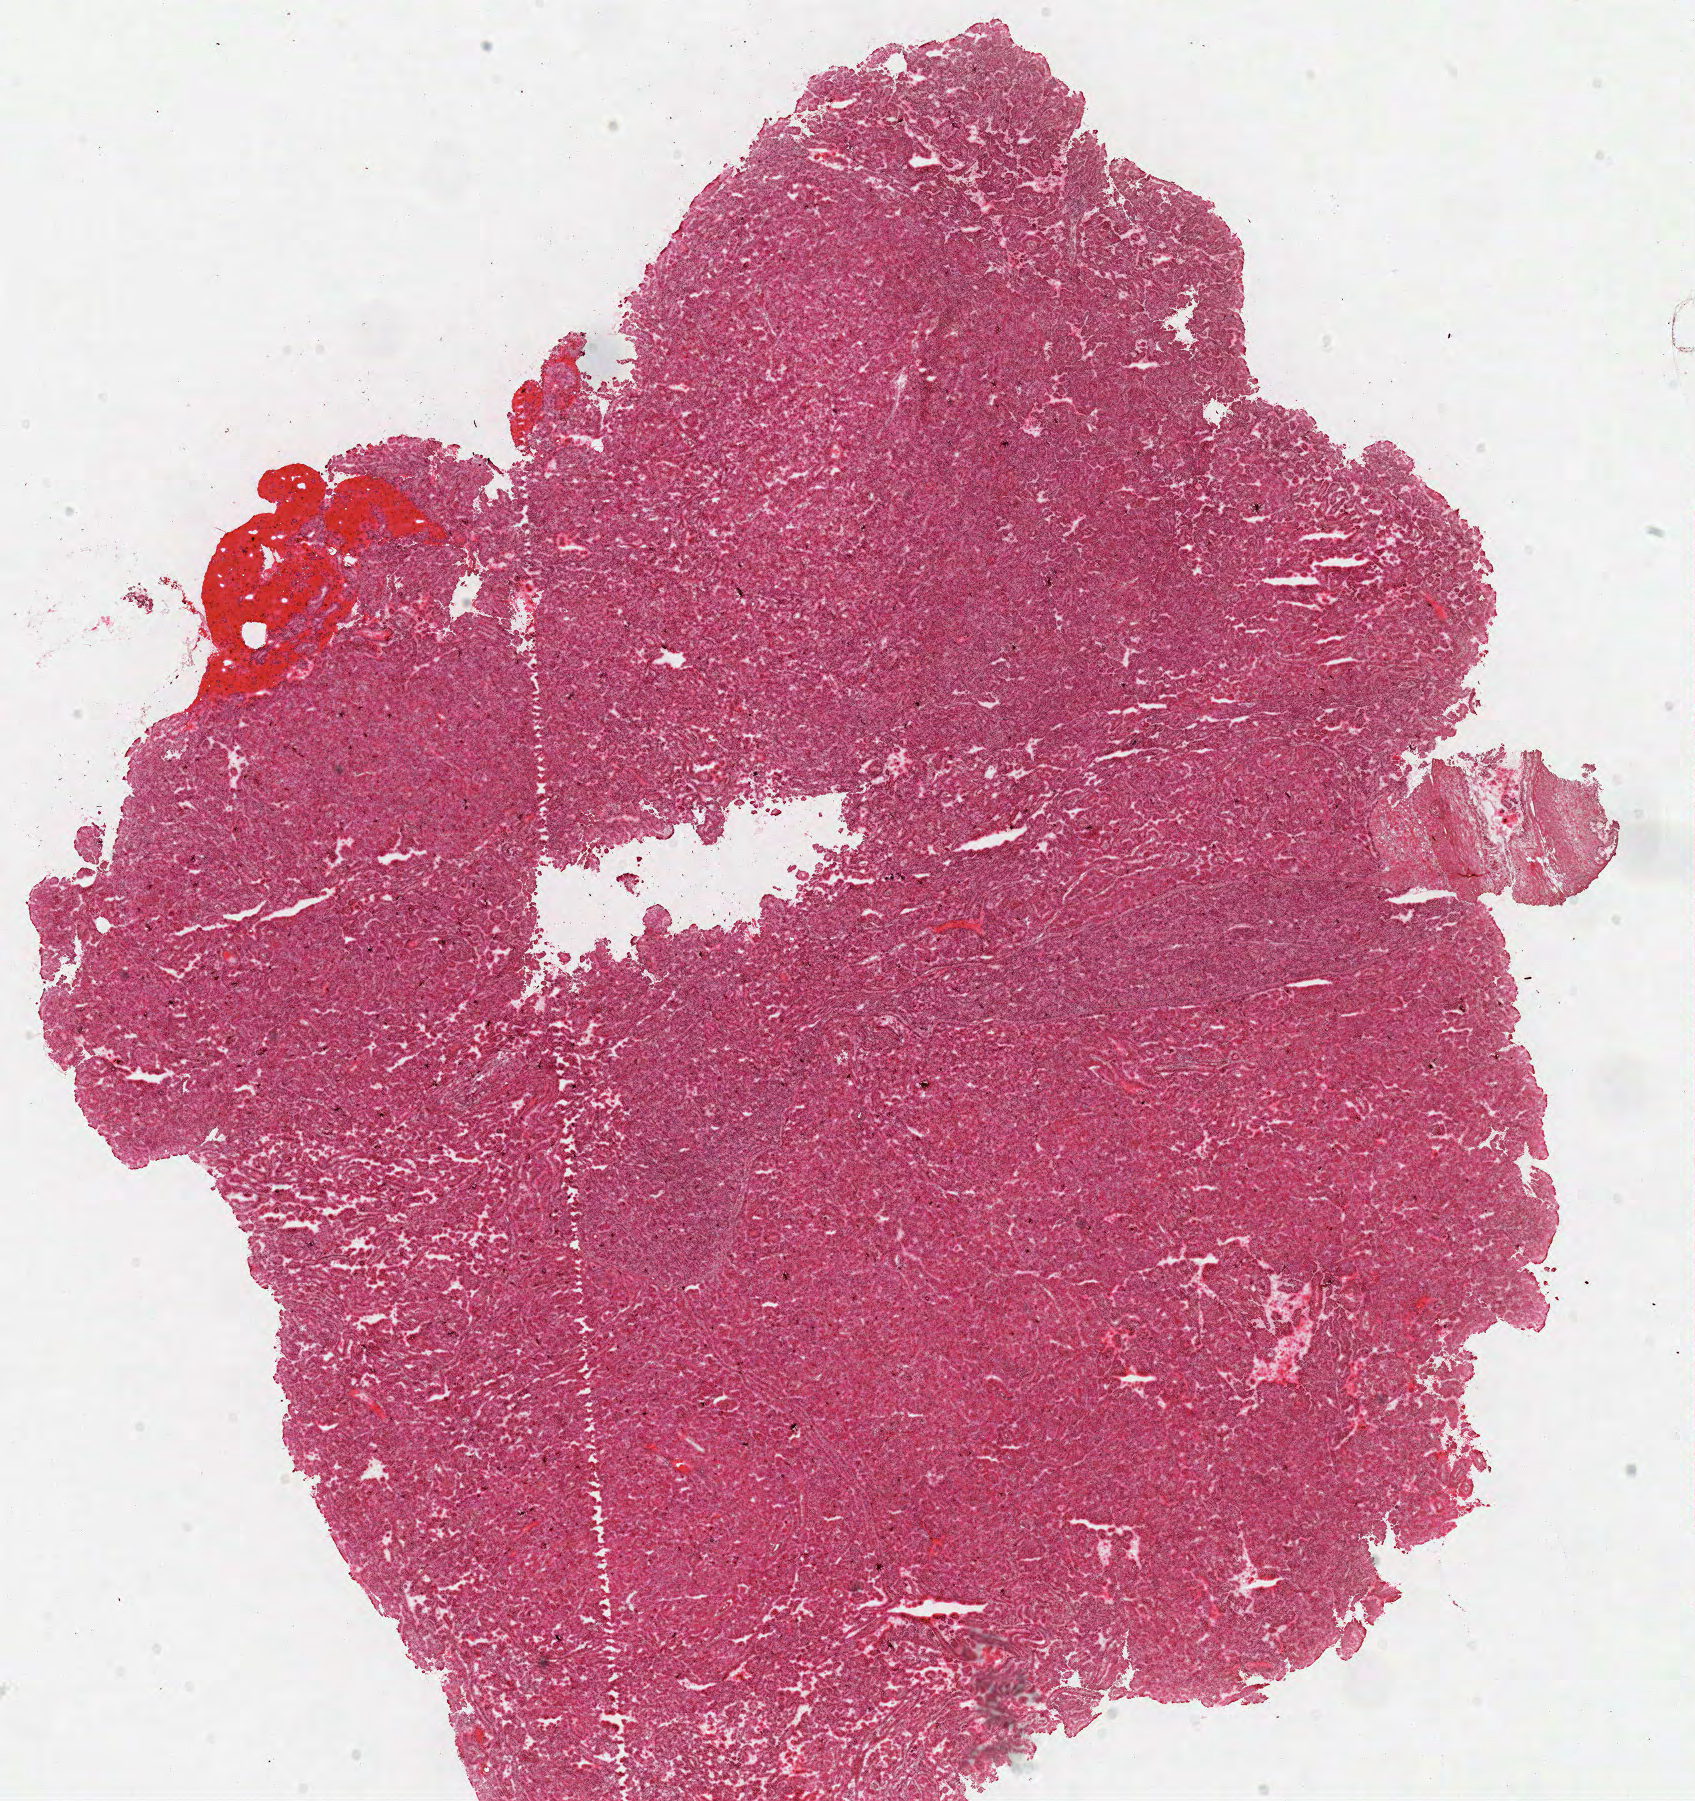
Digitized H&E tissue section (whole slide), shown as a low-resolution overview of the whole scanned area (about 13.4 x 14.2 mm); frozen section from the top of the tissue portion; kidney, primary tumour sample. Female patient; age at initial diagnosis 79 years. Pathologist review of this section (percent, as recorded): tumour cells 95%, tumour nuclei 85%, normal cells 0%, stromal cells 5%, necrosis 0%.
- diagnosis: Papillary adenocarcinoma, NOS
- AJCC pathologic stage: III
- TNM: T3a N1 M0
- laterality: left